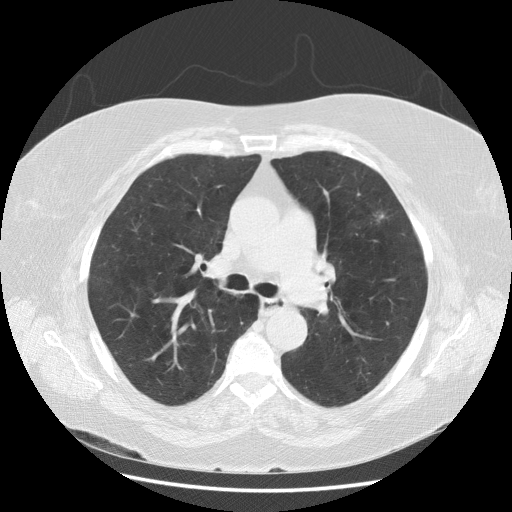
Low-dose screening chest CT, one axial slice. Position 103 of 164 along the scan axis. Reconstruction kernel STANDARD. Lung window (W 1500 / L -600 HU). 2.5 mm slice thickness. 512 × 512 image matrix, field of view 380 × 380 mm.
Outlined on this slice (expert manual segmentation):
- lesion 1 (tumor, upper lobe of left lung): bounding box <380,214,384,219> (left, top, right, bottom; pixels)